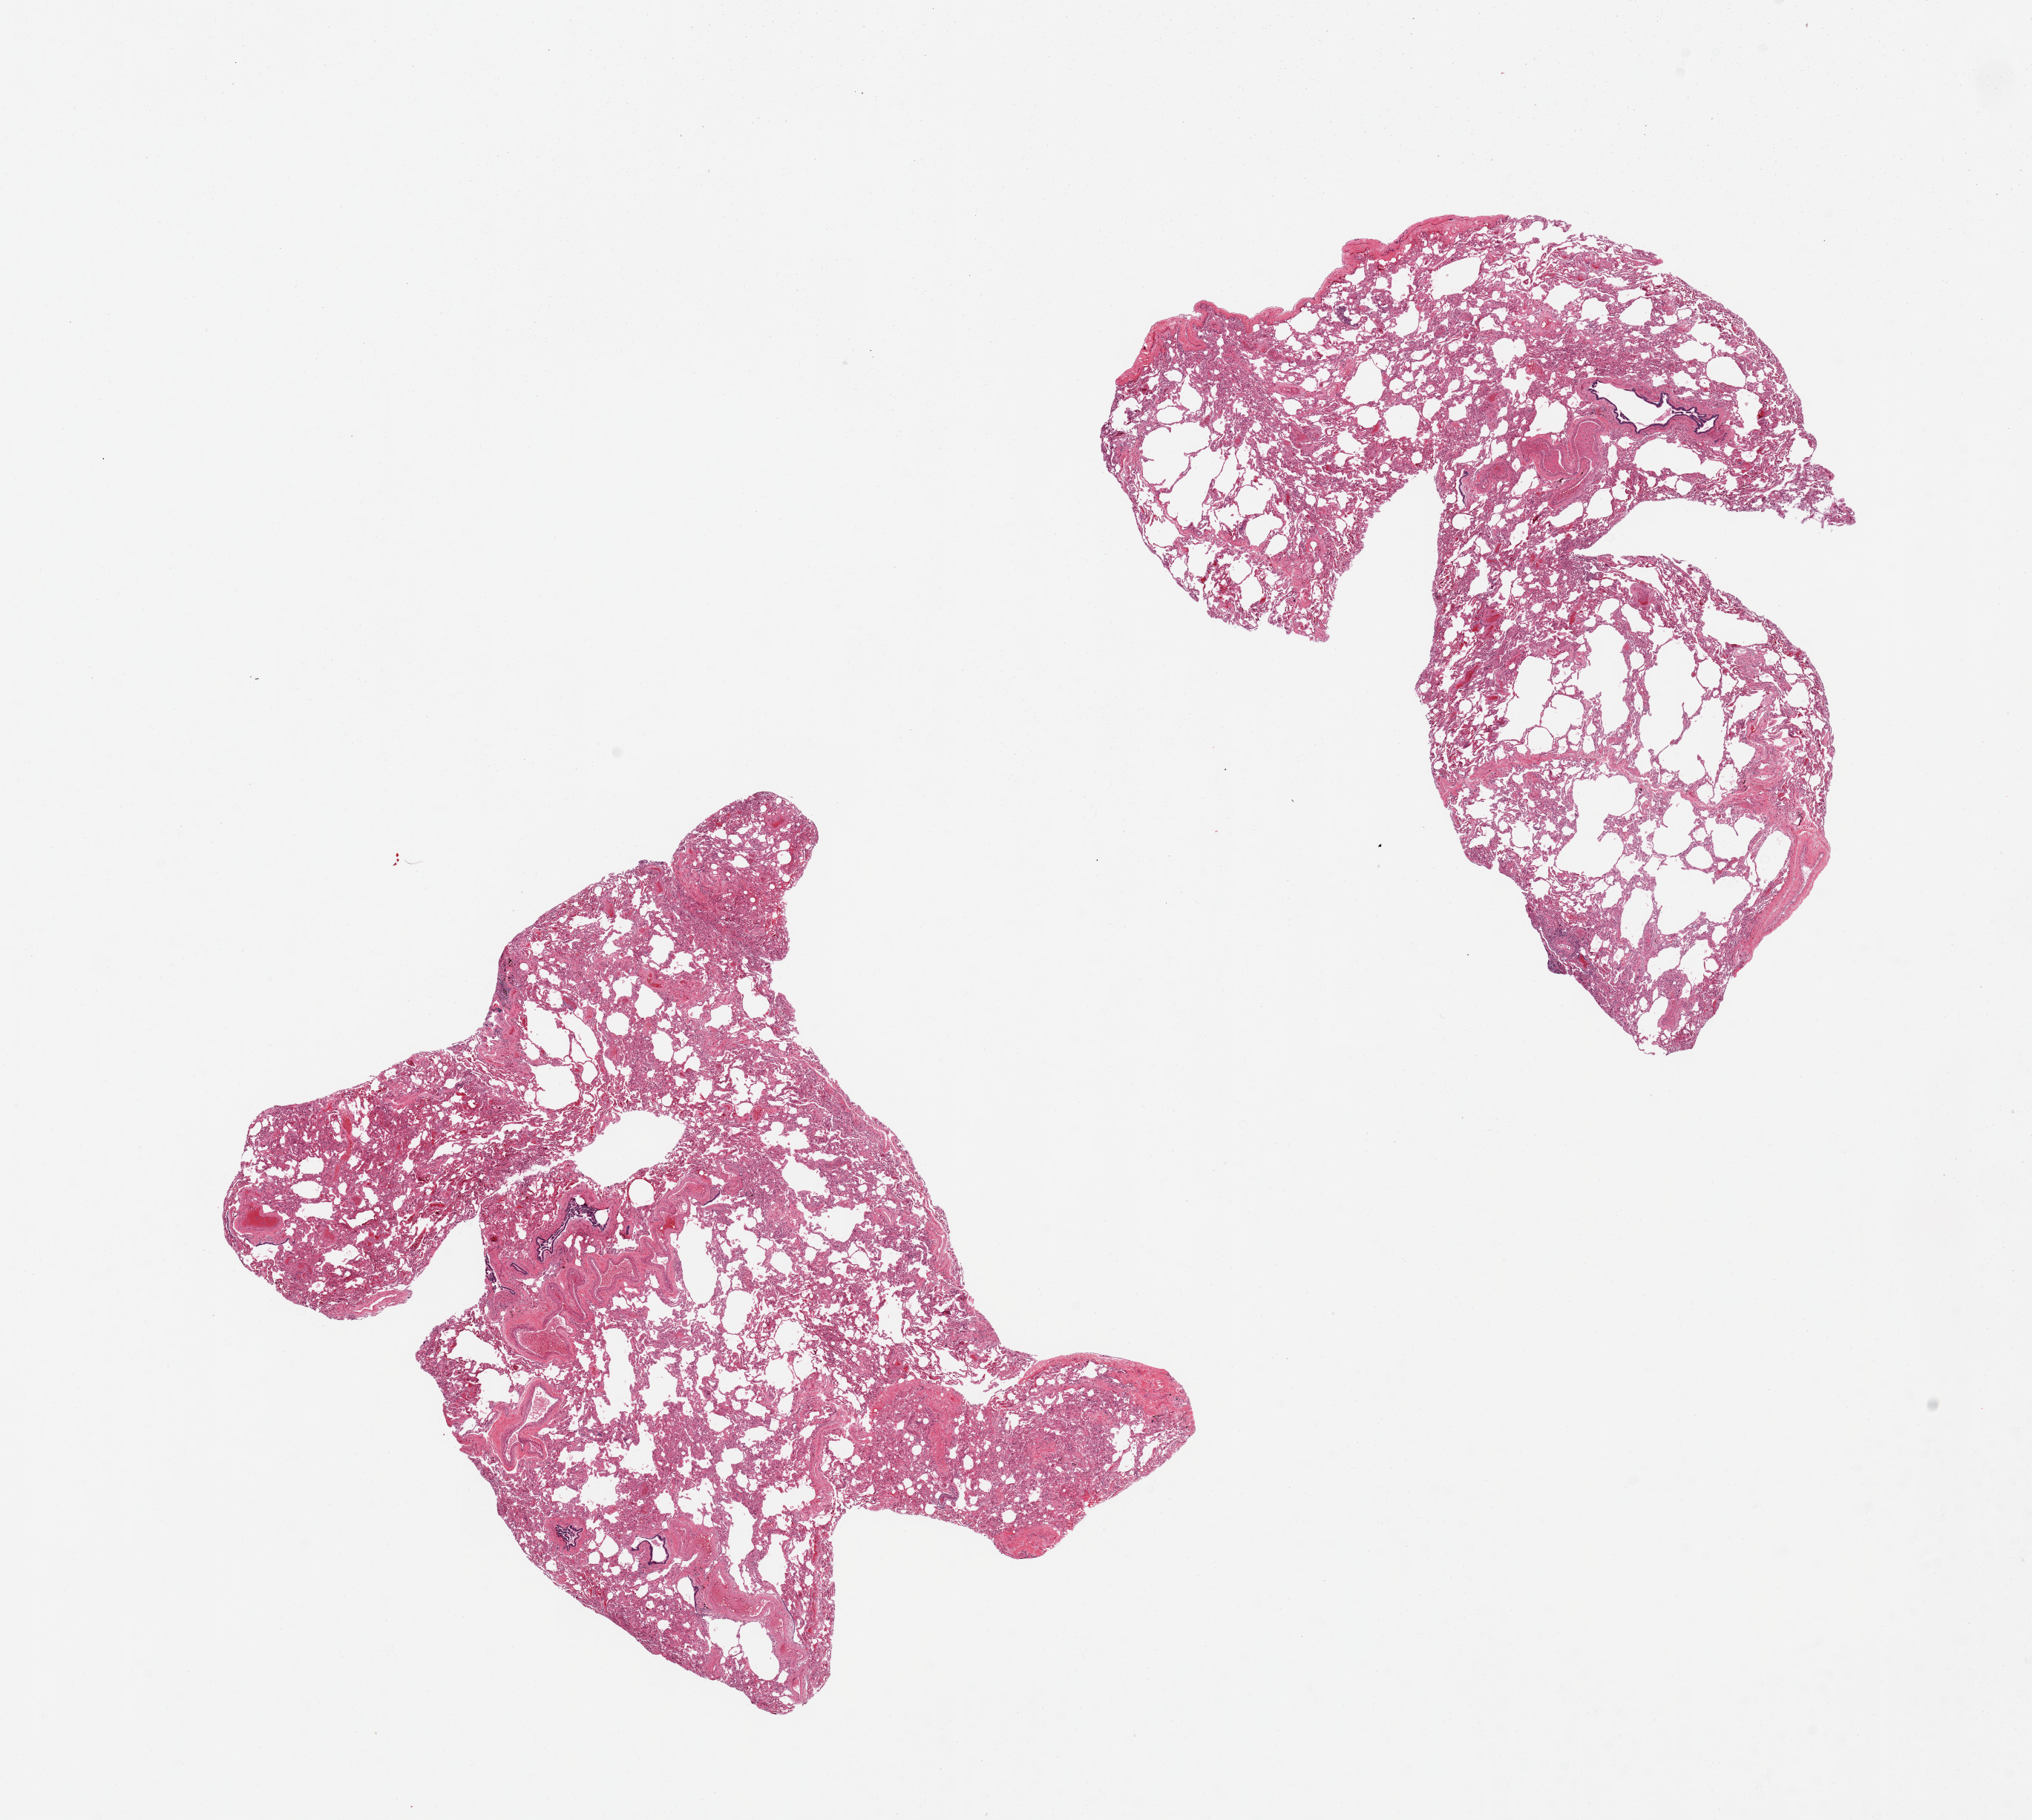
Digitized hematoxylin and eosin (H&E)-stained section — low-resolution overview of the scanned area, about 21.7 x 19.4 mm (from a 20x scan), PAXgene-fixed paraffin-embedded (PFPE) section, section of lung (target tissue), tissue donor sample. Female donor.
Reviewer comment on this tissue sample: 2 pieces, patchy interstitial fibrosis, emphysematous, well preserved bronchial epithelium.